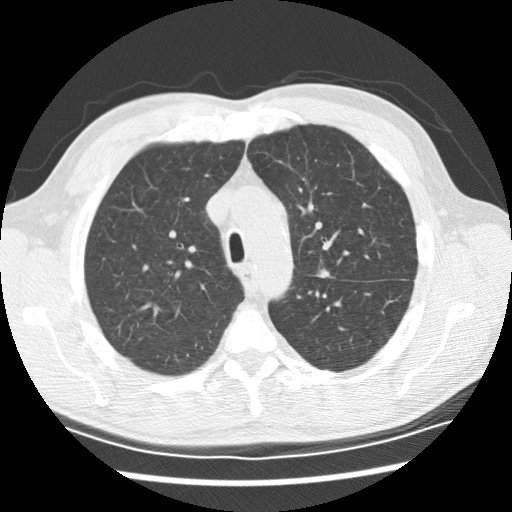
Chest CT (low-dose screening protocol), one axial image; second annual screen; lung window (W 1500 / L -600 HU); 2.5 mm slice thickness; standard (soft-tissue) reconstruction kernel (STANDARD); slice 59 of 208 in the series. Male participant, aged 59 years at enrolment.
Lesion marked by an expert reader, bounding box (x1, y1, x2, y2) in pixels: (306, 259, 343, 294). The exam's reader record, not a measurement of the box and not confirmed to be the same lesion: non-calcified nodule or mass ≥4 mm, left upper lobe, 8 × 7 mm, spiculated (stellate) margins, soft tissue attenuation, pre-existing on the prior screen: yes; interval growth: yes. Later outcome: lung cancer diagnosed 251 days after this screen — adenocarcinoma, NOS, left upper lobe, left lower lobe, poorly differentiated (G3), stage IV (AJCC 6th edition).